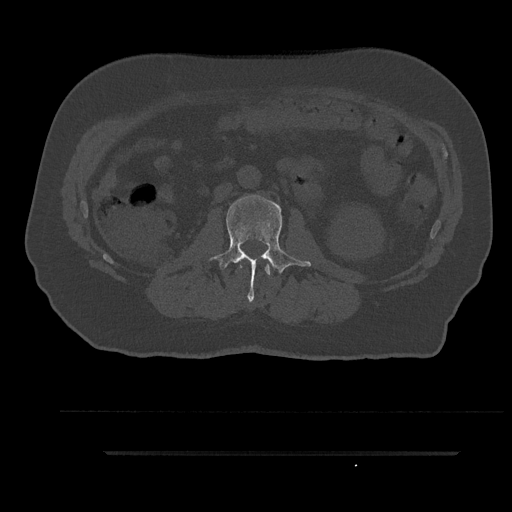
CT including the spine, one axial slice; slice 111 of 797 in the series (ordered by position); 120 kVp; bone window (W 1800 / L 400 HU); 512 × 512 image matrix. Male patient, age 63 years. Case-level facts recorded for this patient, not image findings: primary cancer: renal; vertebrae with lytic lesions (as recorded): T8.
Structures marked on this image (semi-automatically segmented with operator editing):
- L1 vertebra: bounding box [x1, y1, x2, y2] px = [239, 264, 271, 275]
- L2 vertebra: [209, 195, 311, 302]